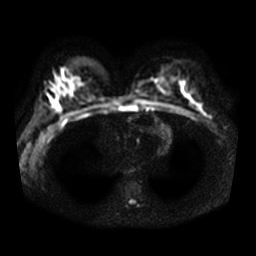
Breast MRI, one axial slice; position 21 of 36 along the scan axis; diffusion-weighted series; image 2 of 4 stored at this slice position (different b-values; order by instance number); 3 T; 256 × 256 image matrix, field of view 340 × 340 mm. Female patient.
Outlined on this slice (outlined manually by an expert reader):
- tumour on diffusion-weighted imaging: bounding box <196,107,201,111> (left, top, right, bottom; pixels)